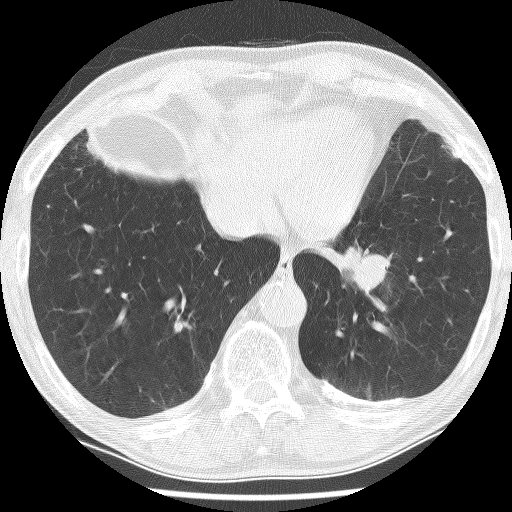
Low-dose screening chest CT, one axial slice; position 44 of 226 along the scan axis; 120 kVp; lung window (W 1500 / L -600 HU); 2.5 mm slice thickness; 512 × 512 image matrix.
Structures marked on this image (manually delineated by an expert):
- lesion 1 (tumor, lower lobe of left lung): bounding box (x1, y1, x2, y2) in pixels: (339, 246, 390, 296)